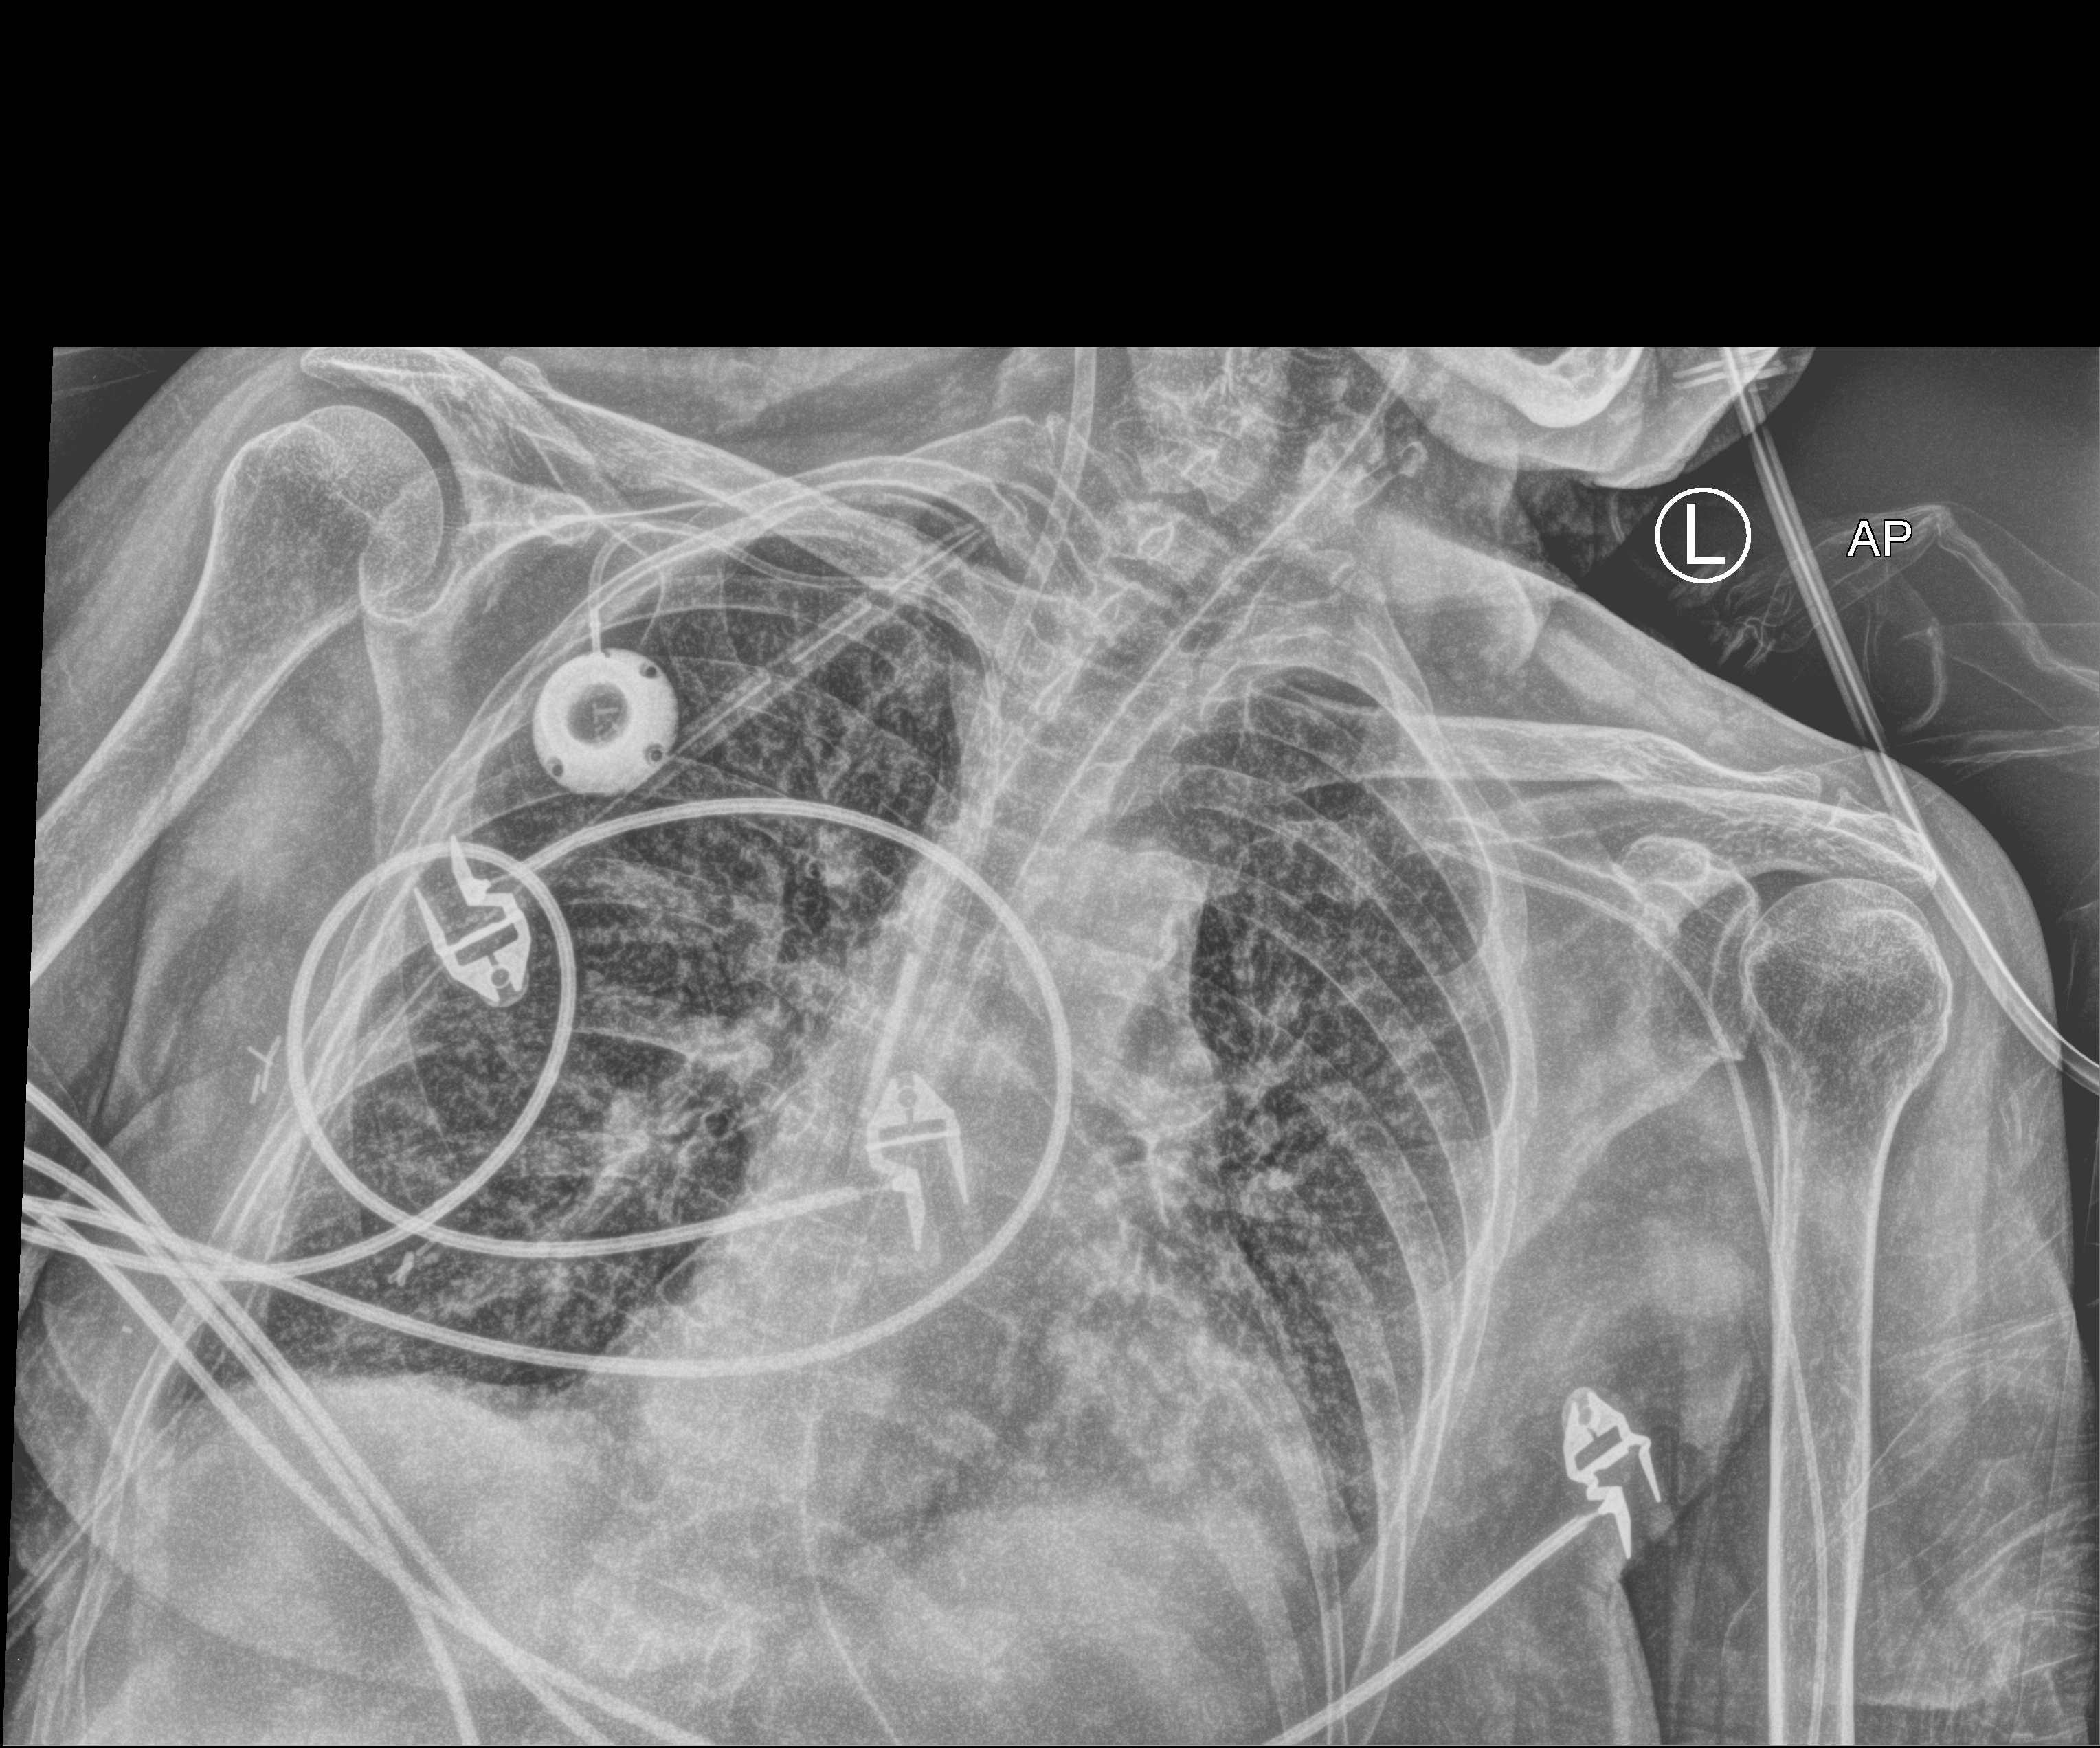
Chest X-ray (portable), anteroposterior (AP) projection. Patient hospitalised with COVID-19; female, aged 60–74 years.
Hospital-stay facts (about this admission, not read from this image; timing relative to this image not recorded):
- diabetes (admission record): no
- chronic kidney disease (admission record): no
- hypertension (admission record): yes